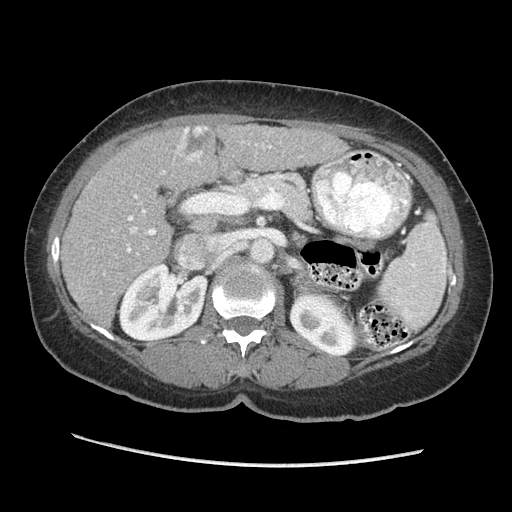
Contrast-enhanced abdominal CT (liver protocol), one axial slice. Position 122 of 170 along the scan axis. Reconstruction kernel STANDARD. 140 kVp. Soft-tissue window (W 400 / L 40 HU). 2.5 mm slice thickness. 512 × 512 image matrix, field of view 360 × 360 mm. Case-level facts recorded for this patient, not image findings: diagnosis: hepatocellular carcinoma (patient treated with transarterial chemoembolisation; whether this scan precedes or follows treatment is not stated here); TNM stage (as recorded): Stage-II.
Structures marked on this image (semi-automatic segmentation, software-assisted and operator-edited):
- liver parenchyma outside the tumour (the mass and vessels are separate outlines, so this box may not span the whole liver): bounding box [x1, y1, x2, y2] px = [62, 124, 347, 324]
- mass: [176, 126, 216, 163]
- liver vessels: [112, 144, 272, 252]